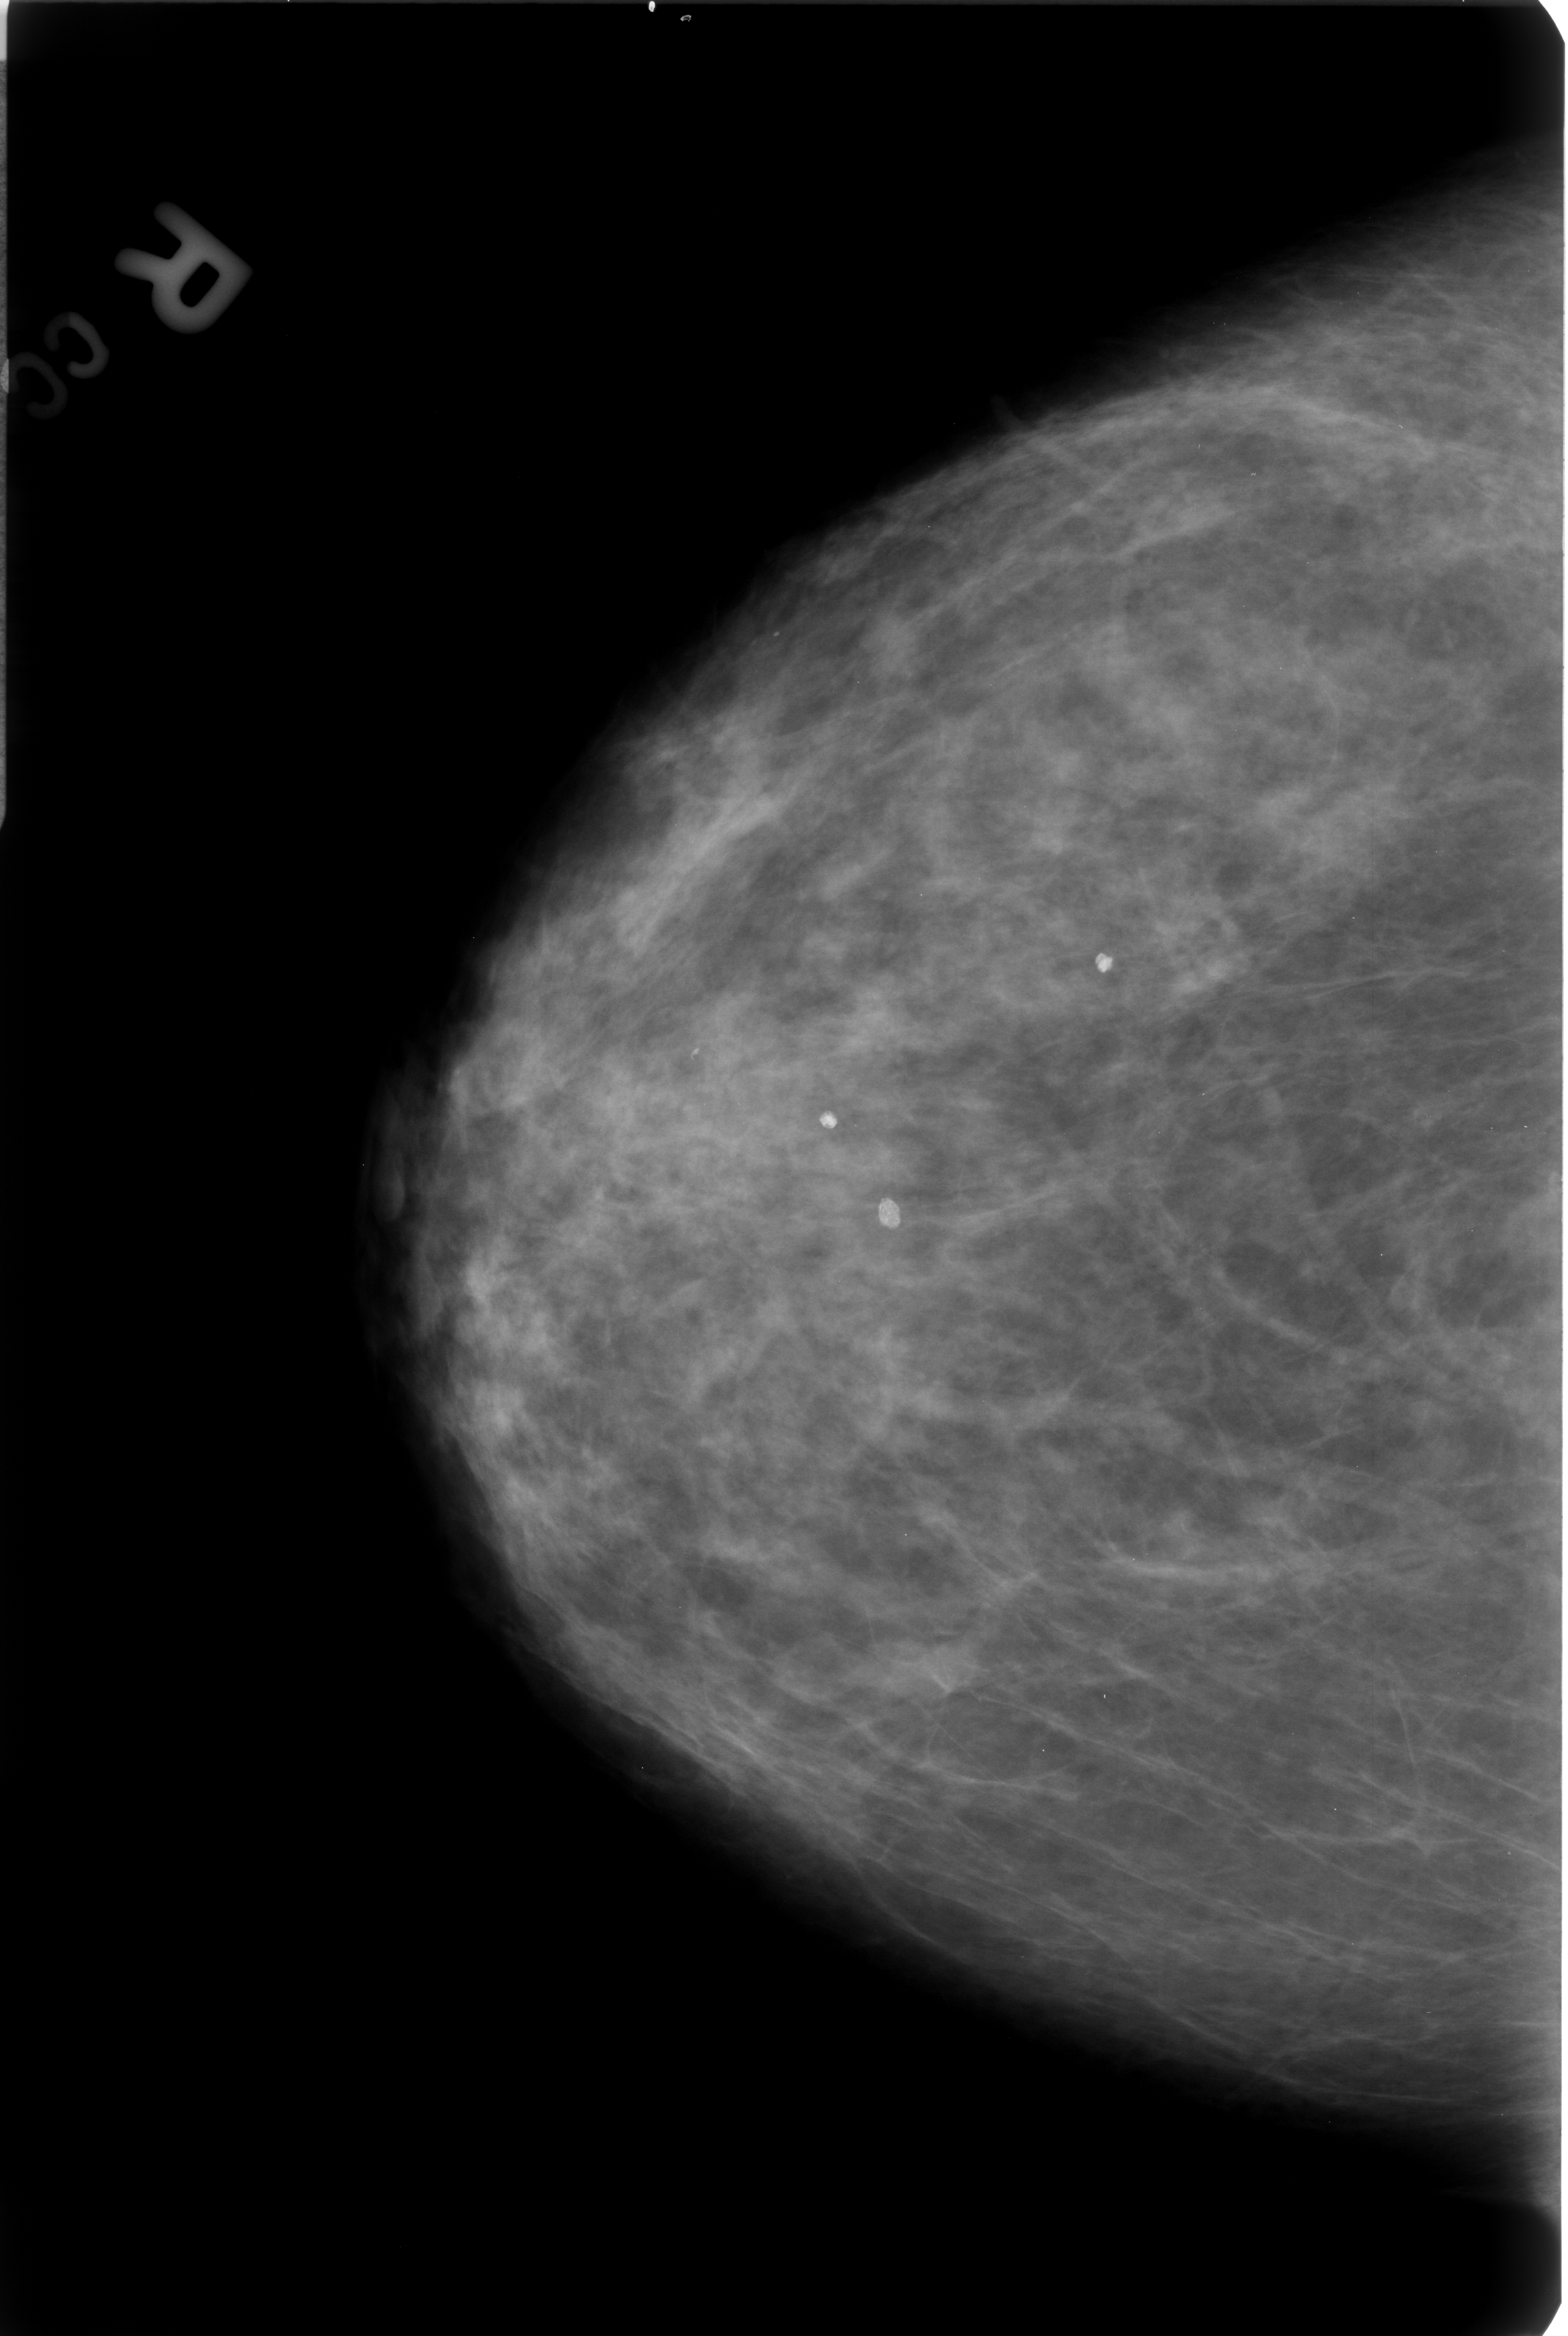
Scanned film-screen mammogram; right breast; craniocaudal (CC) view; BI-RADS breast density category 2 (scale 1–4); 1568 × 2336 image matrix.
Expert-marked regions of interest on this film, with their recorded descriptors:
- Finding 1 of 3: calcifications, morphology coarse / round and regular / lucent center; BI-RADS assessment category 2; subtlety rating 5 on a 1 (subtle) to 5 (obvious) scale; outcome (as recorded, no biopsy): benign without callback (not worked up further): bounding box <820,1107,842,1140> (left, top, right, bottom; pixels)
- Finding 2 of 3: calcifications, morphology coarse / round and regular / lucent center; BI-RADS assessment category 2; outcome (as recorded, no biopsy): benign without callback (not worked up further): <872,1192,910,1238>
- Finding 3 of 3: calcifications, morphology coarse / round and regular / lucent center; BI-RADS assessment category 2; subtlety rating 4 on a 1 (subtle) to 5 (obvious) scale; benign; no additional work-up was recommended (outcome (as recorded, no biopsy): benign without callback): <1091,949,1120,979>